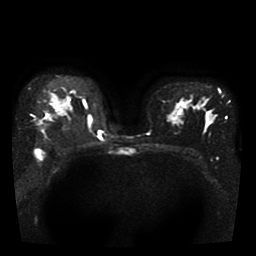
Breast MRI, one axial slice; diffusion-weighted series; image 2 of 4 stored at this slice position (different b-values; order by instance number); 1.5 T; 256 × 256 image matrix, field of view 330 × 330 mm. Female patient.
Annotated regions visible in this slice (outlined manually by an expert reader):
- tumour on diffusion-weighted imaging: bounding box (x1, y1, x2, y2) in pixels: (36, 120, 43, 126)